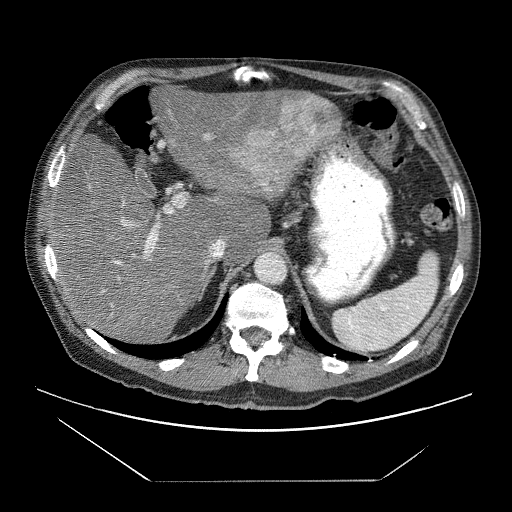
Contrast-enhanced abdominal CT (liver protocol), one axial slice; slice 45 of 83 in the series (ordered by position); reconstruction kernel STANDARD; 120 kVp; soft-tissue window (W 400 / L 40 HU); 2.5 mm slice thickness; 512 × 512 image matrix, field of view 420 × 420 mm. From the clinical record (not read from this slice): diagnosis: hepatocellular carcinoma (patient treated with transarterial chemoembolisation; whether this scan precedes or follows treatment is not stated here); TNM stage (as recorded): Stage-IVB; Child-Pugh class: B; tumour differentiation: poorly differentiated; tumour nodularity: uninodular.
Structures marked on this image (semi-automatic segmentation, software-assisted and operator-edited):
- liver parenchyma outside the tumour (the mass and vessels are separate outlines, so this box may not span the whole liver): box from (x=50, y=74) to (x=340, y=340) px
- mass: (x=233, y=92)–(x=341, y=189)
- liver vessels: (x=54, y=134)–(x=271, y=306)